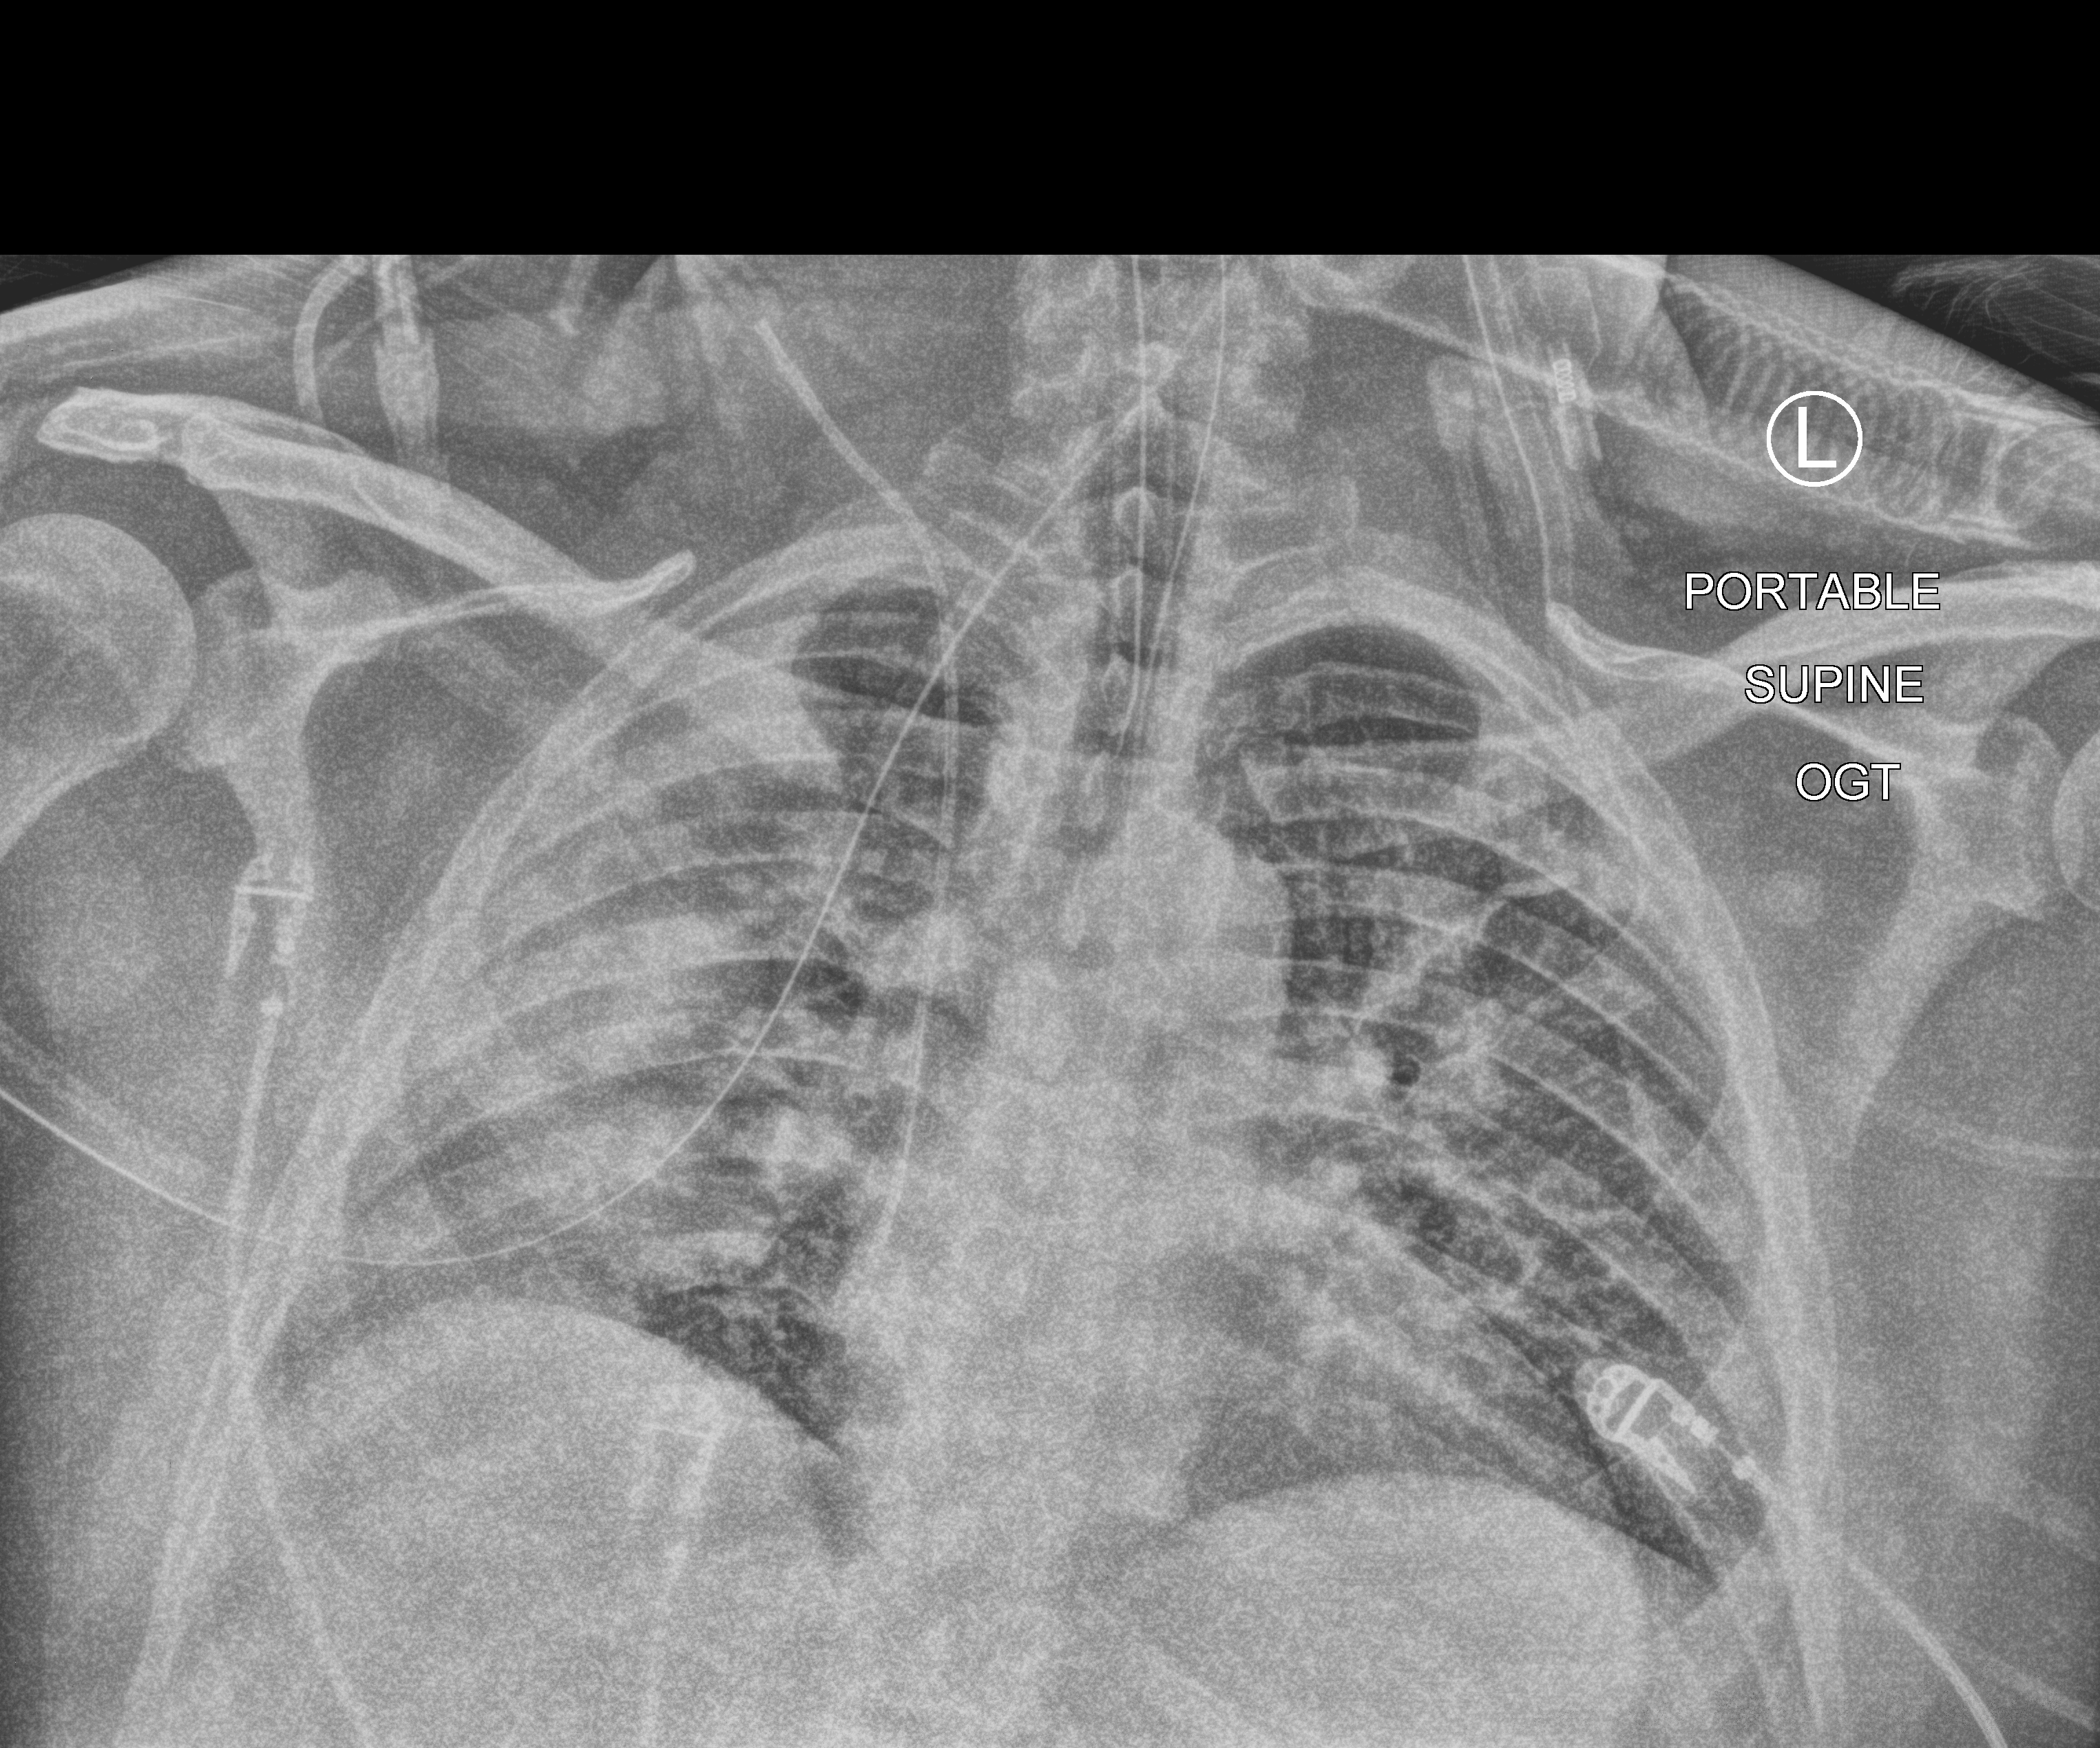
Portable chest radiograph; anteroposterior (AP) projection. Male patient hospitalised with COVID-19, age 18–59 years.
Admission-level facts for this patient (not findings on this image; timing relative to this image not recorded): mechanically ventilated during this hospital stay: yes.